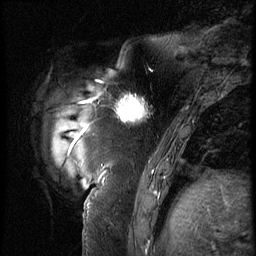
Breast MRI (dynamic contrast-enhanced), one sagittal slice; position 14 of 62 along the scan axis; 3 images stored at this slice position (order not interpretable as contrast timing); 1.5 T; TE 4.2 ms, TR 9 ms; 2.5 mm slice thickness; 256 × 256 image matrix, field of view 180 × 180 mm. Patient: female, 57 years. From the clinical record (not read from this slice): setting: breast cancer imaged before/during neoadjuvant chemotherapy; receptor status: triple-negative.
Structures marked on this image (semi-automatically segmented with operator editing):
- analysis volume of interest (the breast-tissue region the enhancement analysis was run in; not a lesion): bounding box [x1, y1, x2, y2] px = [105, 84, 158, 135]
- tumour enhancement mask (voxels above the 140 % enhancement threshold inside the analysis volume of interest): [116, 94, 149, 123]